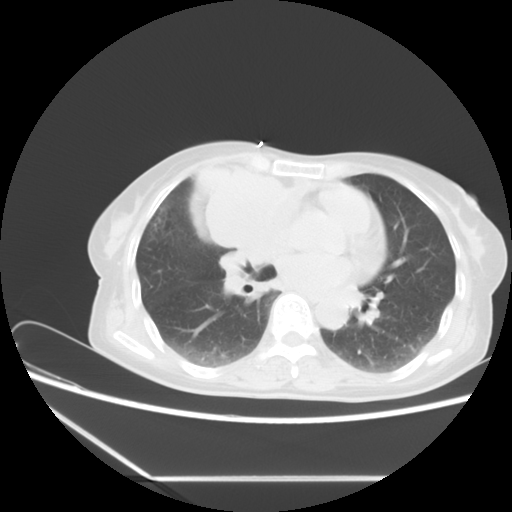
Chest CT, one axial slice. Slice 4 of 16 in the series (ordered by position). Reconstruction kernel STANDARD. 120 kVp. Lung window (W 1500 / L -600 HU). 5 mm slice thickness. 512 × 512 image matrix. Patient: female, 63 years. From the clinical record (not read from this slice): clinical TNM (as recorded): T2b N1 M0.
Structures marked on this image (bounding box drawn by a radiologist):
- lung tumour (recorded histology: adenocarcinoma): bounding box <194,156,298,253> (left, top, right, bottom; pixels)